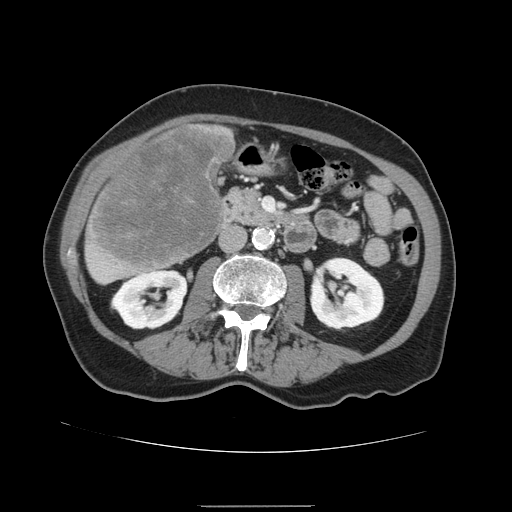
Contrast-enhanced abdominal CT, one axial slice. Position 47 of 168 along the scan axis. 120 kVp. Intravenous contrast given. Soft-tissue window (W 400 / L 40 HU). 512 × 512 image matrix, field of view 386 × 386 mm. Male patient, age 74 years. From the clinical record (not read from this slice): diagnosis: colorectal cancer liver metastases, imaged before liver resection; multiple liver metastases: no; largest metastasis: 14.5 cm.
Structures marked on this image (outlined manually by an expert reader):
- liver: bounding box <84,122,236,285> (left, top, right, bottom; pixels)
- liver metastasis: <90,127,233,269>